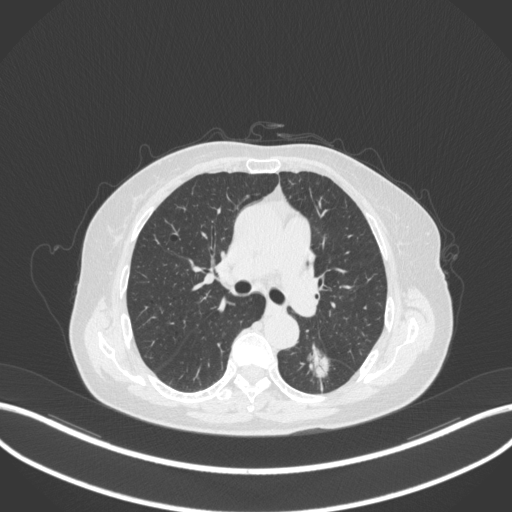
Chest CT, one axial slice. Slice 181 of 352 in the series (ordered by position). Lung window (W 1500 / L -600 HU). 1 mm slice thickness. 512 × 512 image matrix. Female patient, age 70 years. Case-level facts recorded for this patient, not image findings: clinical TNM (as recorded): T1c N0 M0.
Annotated regions visible in this slice (rectangle marked by the reading radiologist):
- lung tumour (recorded histology: adenocarcinoma): bounding box <299,343,333,383> (left, top, right, bottom; pixels)